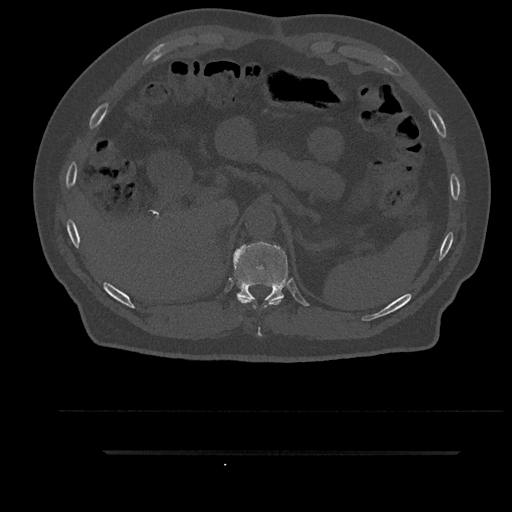
CT including the spine, one axial slice. Position 330 of 797 along the scan axis. Reconstruction kernel Br40s/3. Bone window (W 1800 / L 400 HU). 0.5 mm slice thickness. 512 × 512 image matrix, field of view 432 × 432 mm. Patient: male, 63 years. From the clinical record (not read from this slice): primary cancer: renal; vertebrae with lytic lesions (as recorded): T8.
Structures marked on this image (semi-automatic segmentation, software-assisted and operator-edited):
- T10 vertebra: bounding box [x1, y1, x2, y2] px = [237, 297, 284, 337]
- T11 vertebra: [233, 241, 288, 302]